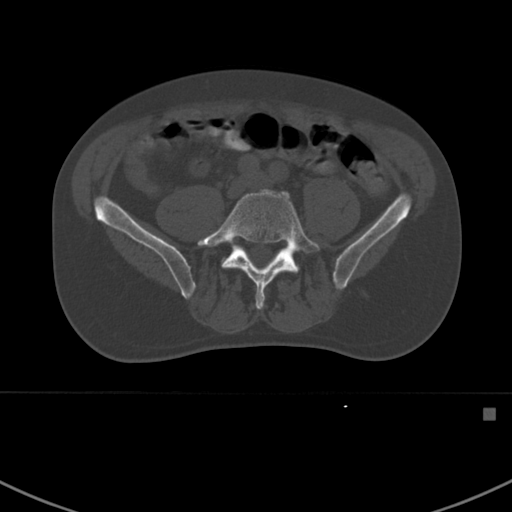
CT including the spine, one axial slice; reconstruction kernel Br40s; bone window (W 1800 / L 400 HU); 512 × 512 image matrix. Patient: male, 59 years. Case-level facts recorded for this patient, not image findings: primary cancer: prostate.
Structures marked on this image (semi-automatic segmentation, software-assisted and operator-edited):
- L5 vertebra: bounding box <197,189,320,310> (left, top, right, bottom; pixels)